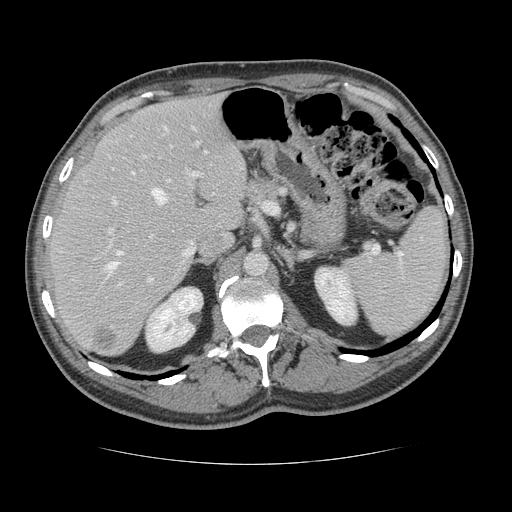
Contrast-enhanced abdominal CT, one axial slice. Slice 85 of 134 in the series (ordered by position). Reconstruction kernel STANDARD. Intravenous contrast given. Soft-tissue window (W 400 / L 40 HU). 2.5 mm slice thickness. 512 × 512 image matrix, field of view 377 × 377 mm. Male patient, age 68 years. From the clinical record (not read from this slice): diagnosis: colorectal cancer liver metastases, imaged before liver resection; multiple liver metastases: yes; largest metastasis: 2.2 cm; disease in both lobes: no.
Annotated regions visible in this slice (expert manual segmentation):
- hepatic veins: bounding box <106,127,213,277> (left, top, right, bottom; pixels)
- liver: <50,96,248,355>
- planned liver remnant (the part of the liver to remain after resection): <50,96,248,337>
- portal vein (with intrahepatic branches): <108,126,204,282>
- liver metastasis: <93,328,116,351>